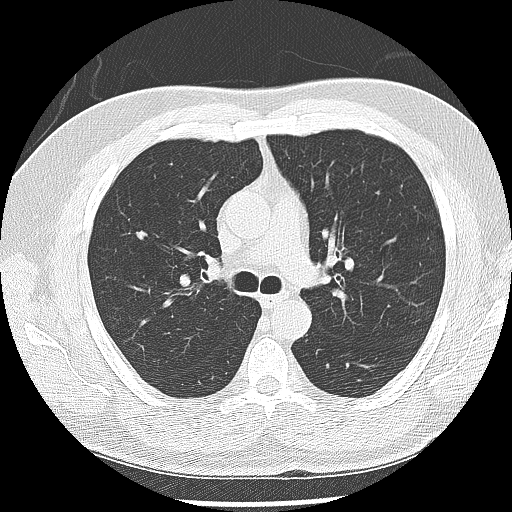
Low-dose screening chest CT, one axial slice. Position 174 of 265 along the scan axis. Reconstruction kernel LUNG. Lung window (W 1500 / L -600 HU). 2.5 mm slice thickness. 512 × 512 image matrix.
Outlined on this slice (outlined manually by an expert reader):
- lesion 1 (tumor, upper lobe of right lung): bounding box <136,230,148,240> (left, top, right, bottom; pixels)